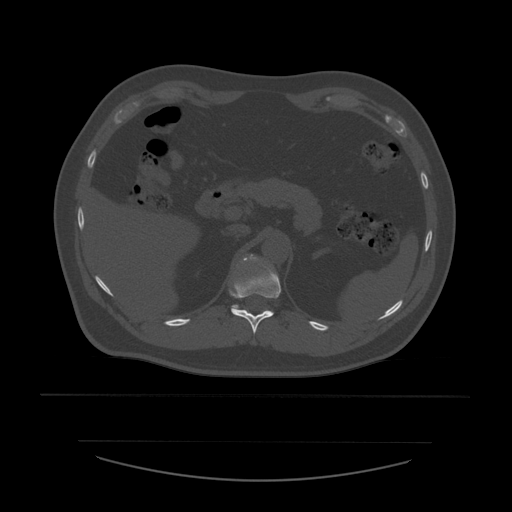
CT including the spine, one axial slice; position 269 of 532 along the scan axis; reconstruction kernel STANDARD; 120 kVp; bone window (W 1800 / L 400 HU); 512 × 512 image matrix, field of view 441 × 441 mm. Patient age 44 years. Case-level facts recorded for this patient, not image findings: primary cancer: soft tissue sarcoma.
Annotated regions visible in this slice (semi-automatically segmented with operator editing):
- T11 vertebra: bounding box <232,262,281,334> (left, top, right, bottom; pixels)
- T12 vertebra: <230,255,256,308>